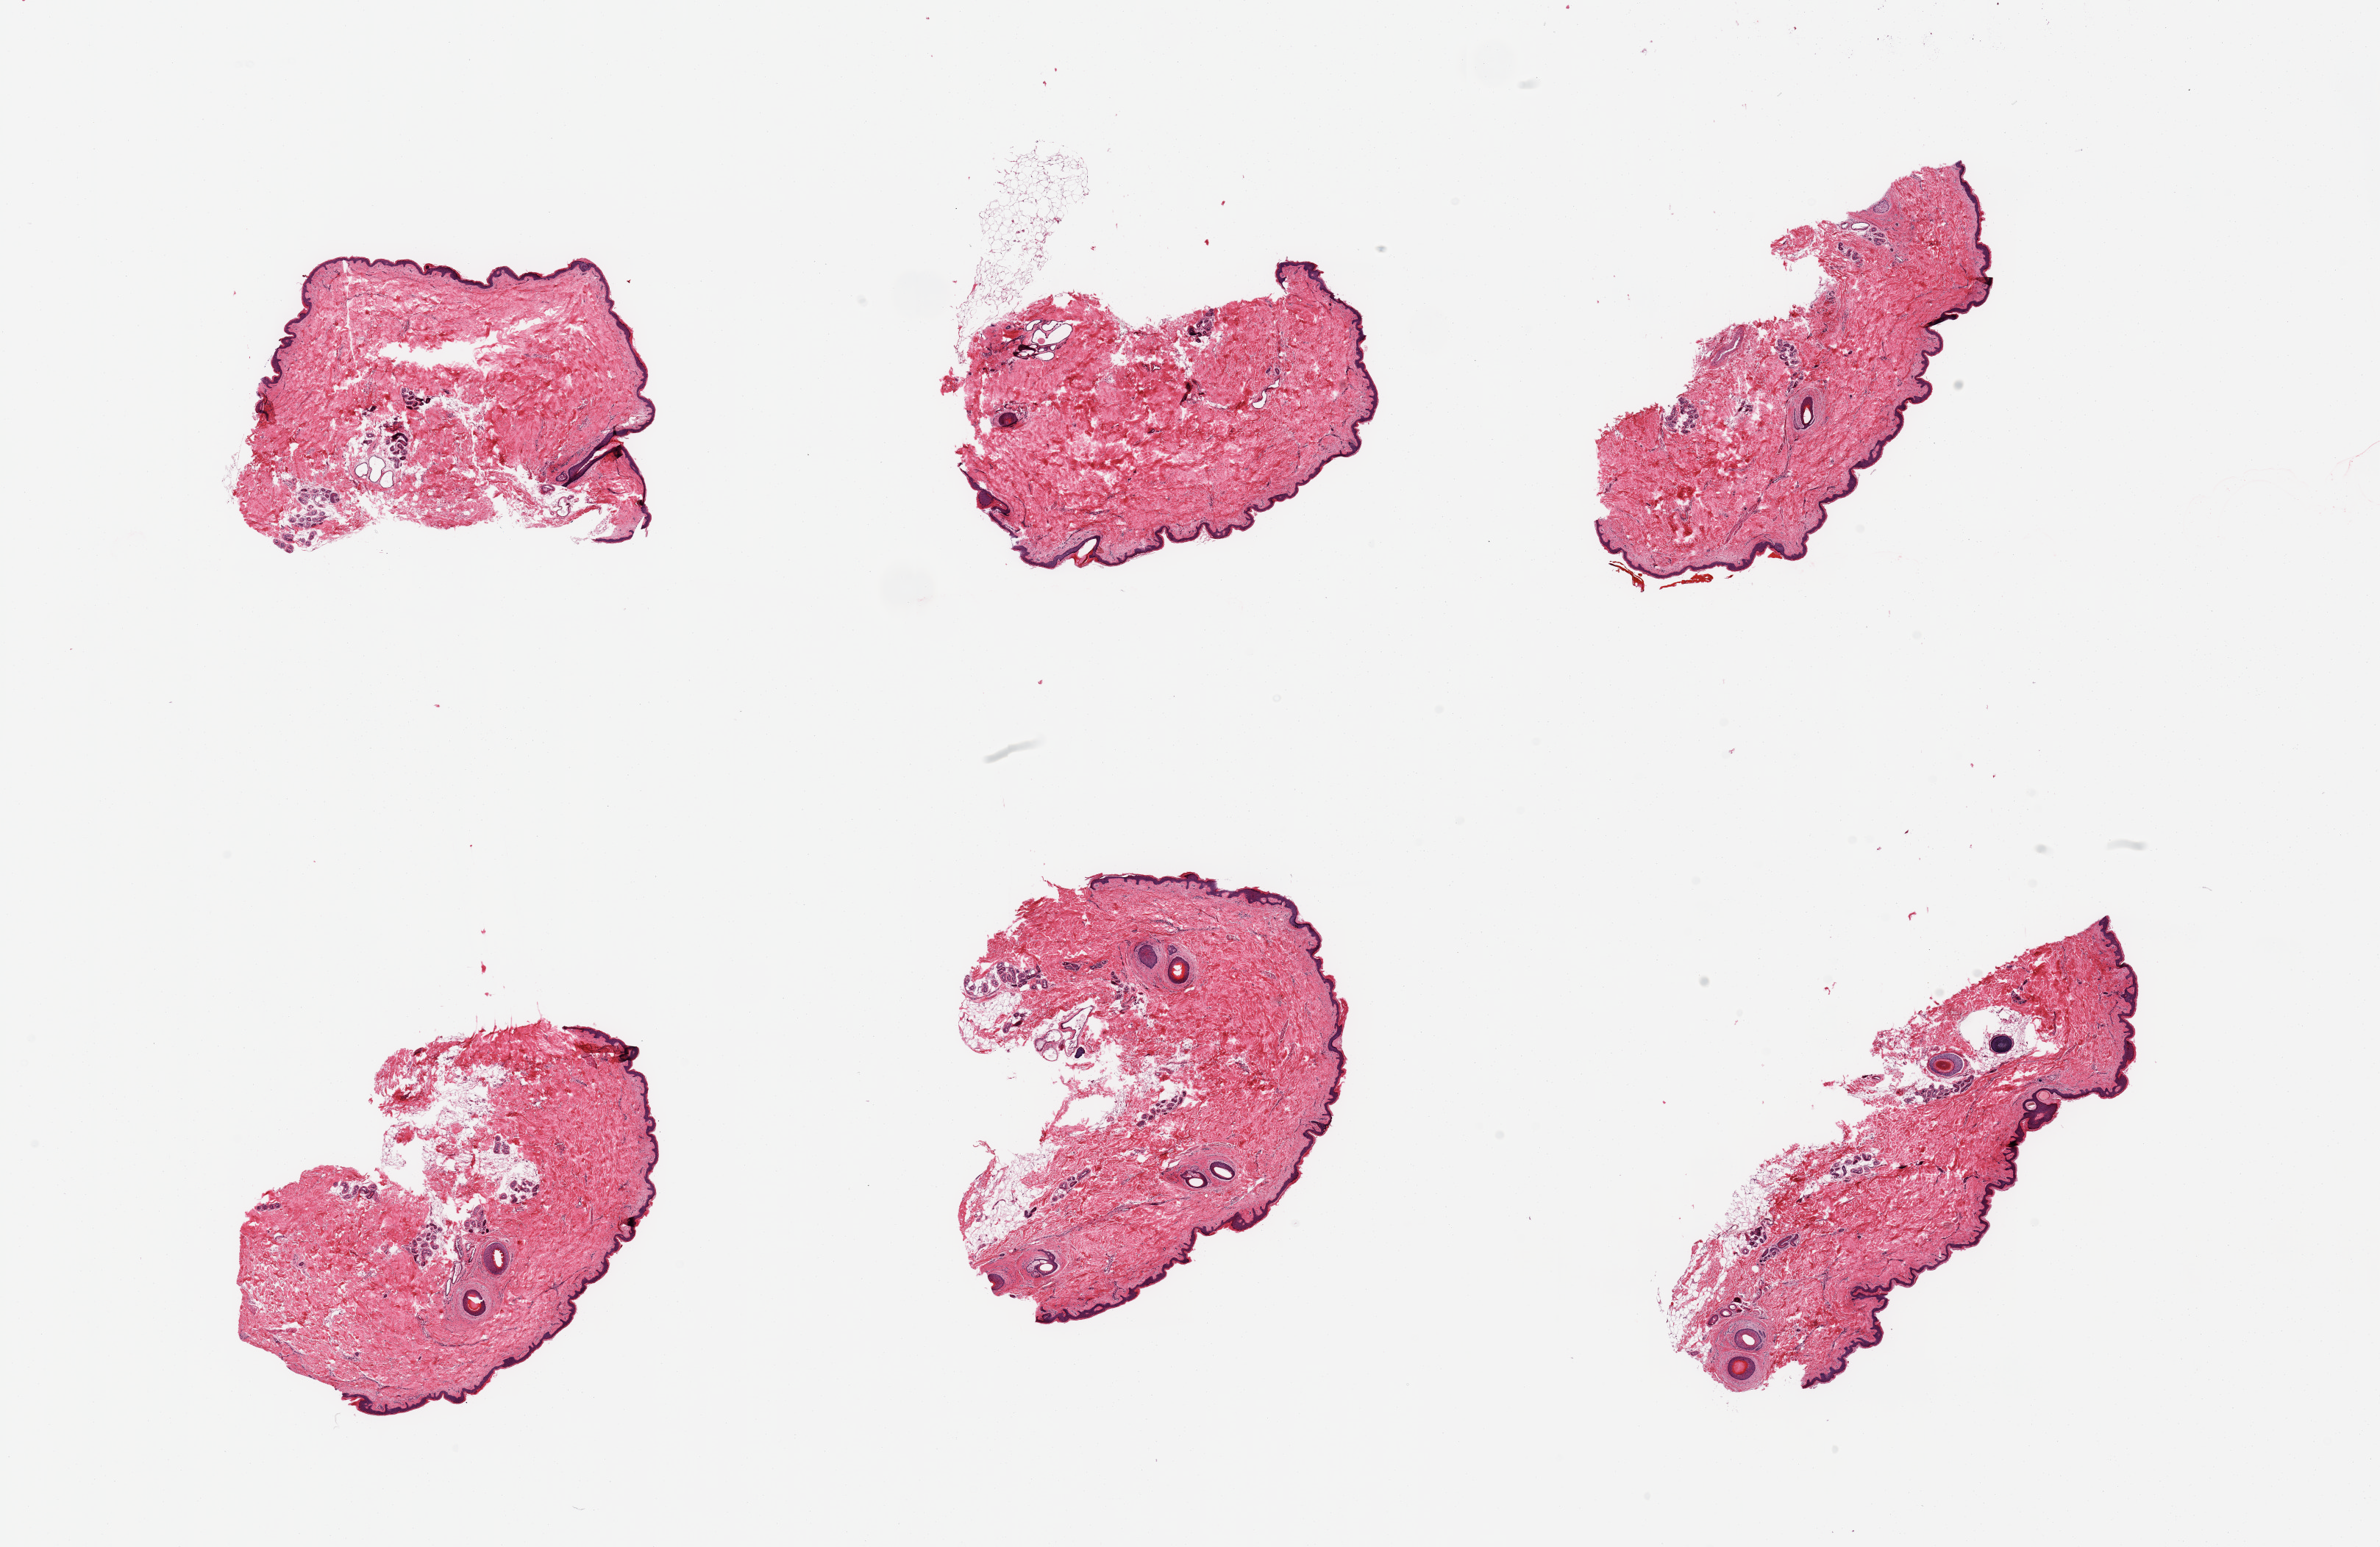
Whole-slide image, hematoxylin and eosin (H&E) stain, brightfield — whole scanned area (about 25.6 x 16.6 mm) shown as a low-resolution overview, PAXgene-fixed paraffin-embedded (PFPE) section, target tissue: skin of suprapubic region, donor tissue sample. Donor: female.
• pathologist's review note for this sample: 6 pieces, no significant dermal fat; squamous epithelium is ~40-45 microns